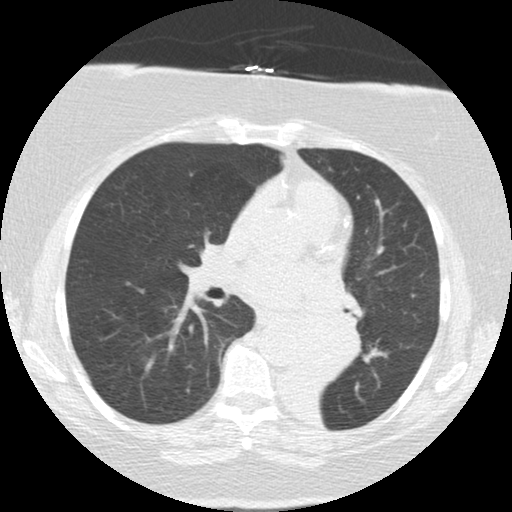
Axial slice from a low-dose chest CT screening exam; baseline annual screen; lung window (W 1500 / L -600 HU); 2.5 mm slice thickness; standard (soft-tissue) reconstruction kernel (STANDARD); 512 × 512 image matrix, field of view 309 × 309 mm. Female, age 71 years at enrolment. Former smoker at enrolment.
Expert-annotated lung lesion, box from (x=286, y=307) to (x=364, y=383) px. The exam's reader record, not a measurement of the box and not confirmed to be the same lesion: non-calcified nodule or mass ≥4 mm, right middle lobe, 5 × 5 mm, smooth margins, soft tissue attenuation. Note: the box lies in the patient's left hemithorax on this image, whereas the reader's record names the right lung; they may be different findings. Later outcome: lung cancer diagnosed 46 days after this screen — large cell carcinoma, NOS, left lower lobe, mediastinum, other location, poorly differentiated (G3), stage IV (AJCC 6th edition), 50 mm at pathology.